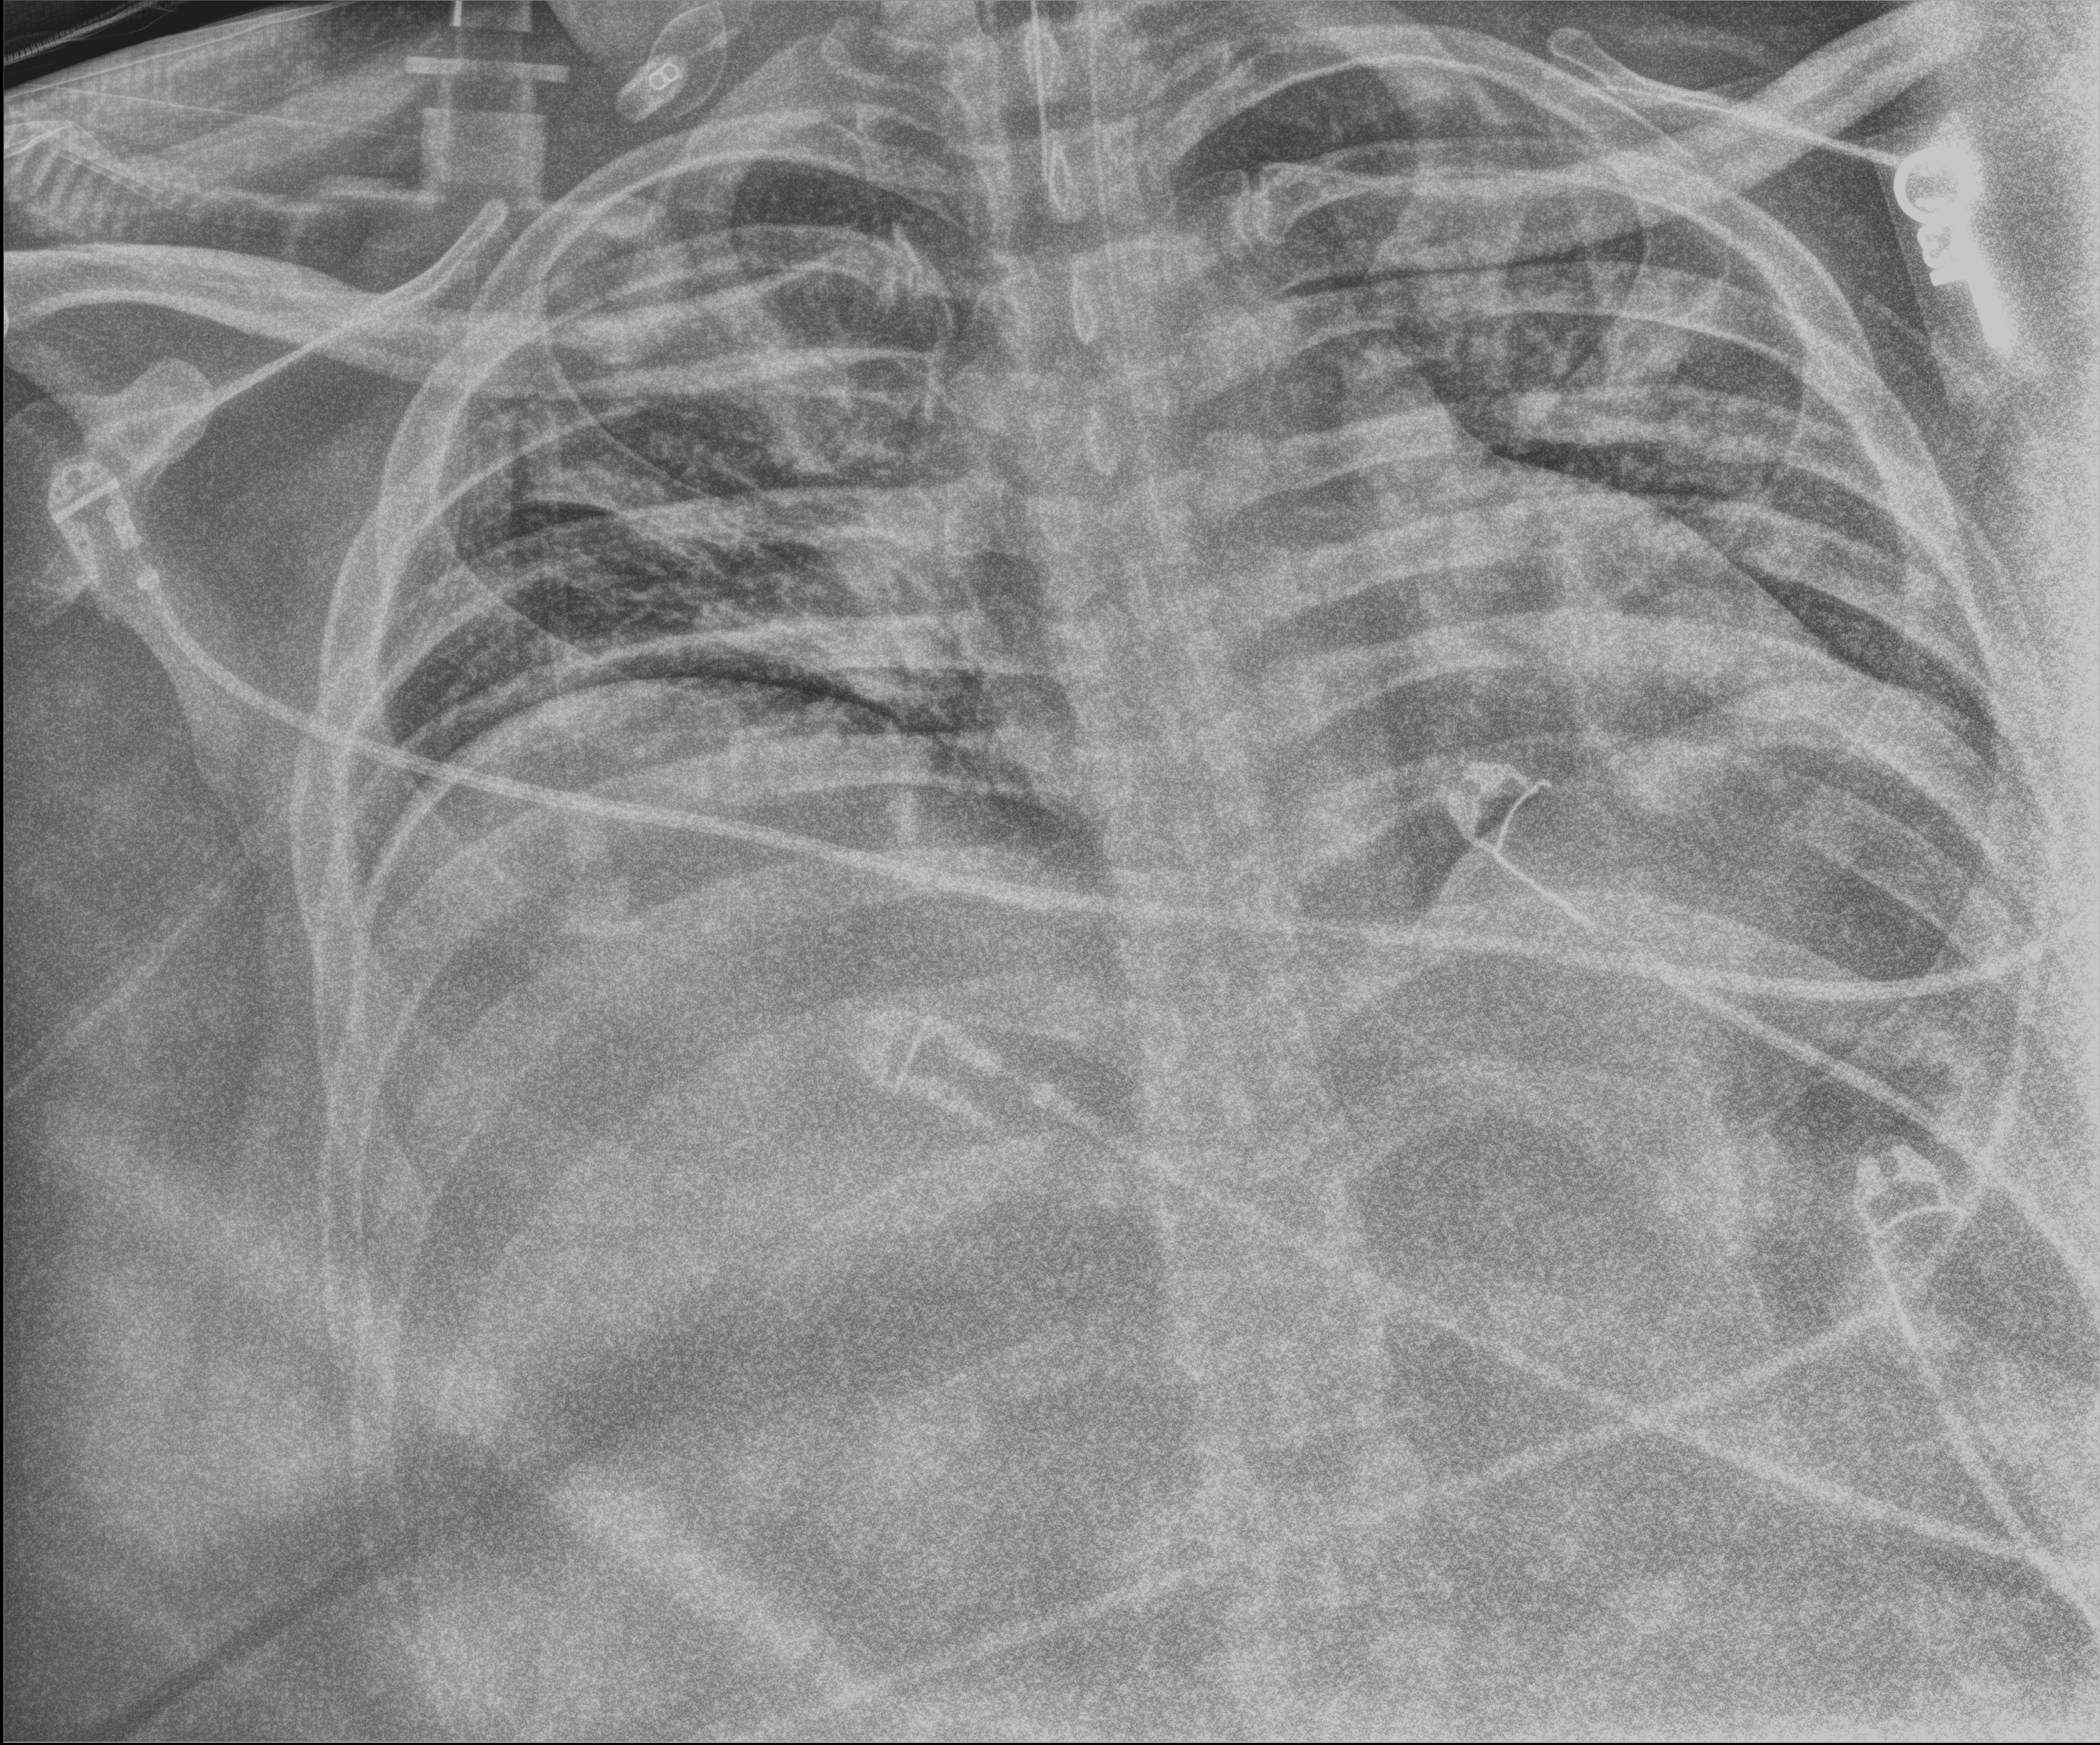
Bedside chest radiograph (digital radiography), anteroposterior (AP) projection. Male patient hospitalised with COVID-19, age 18–59 years.
Admission-level facts for this patient (not findings on this image; timing relative to this image not recorded): mechanically ventilated during this hospital stay: yes; other chronic lung disease (admission record): yes.